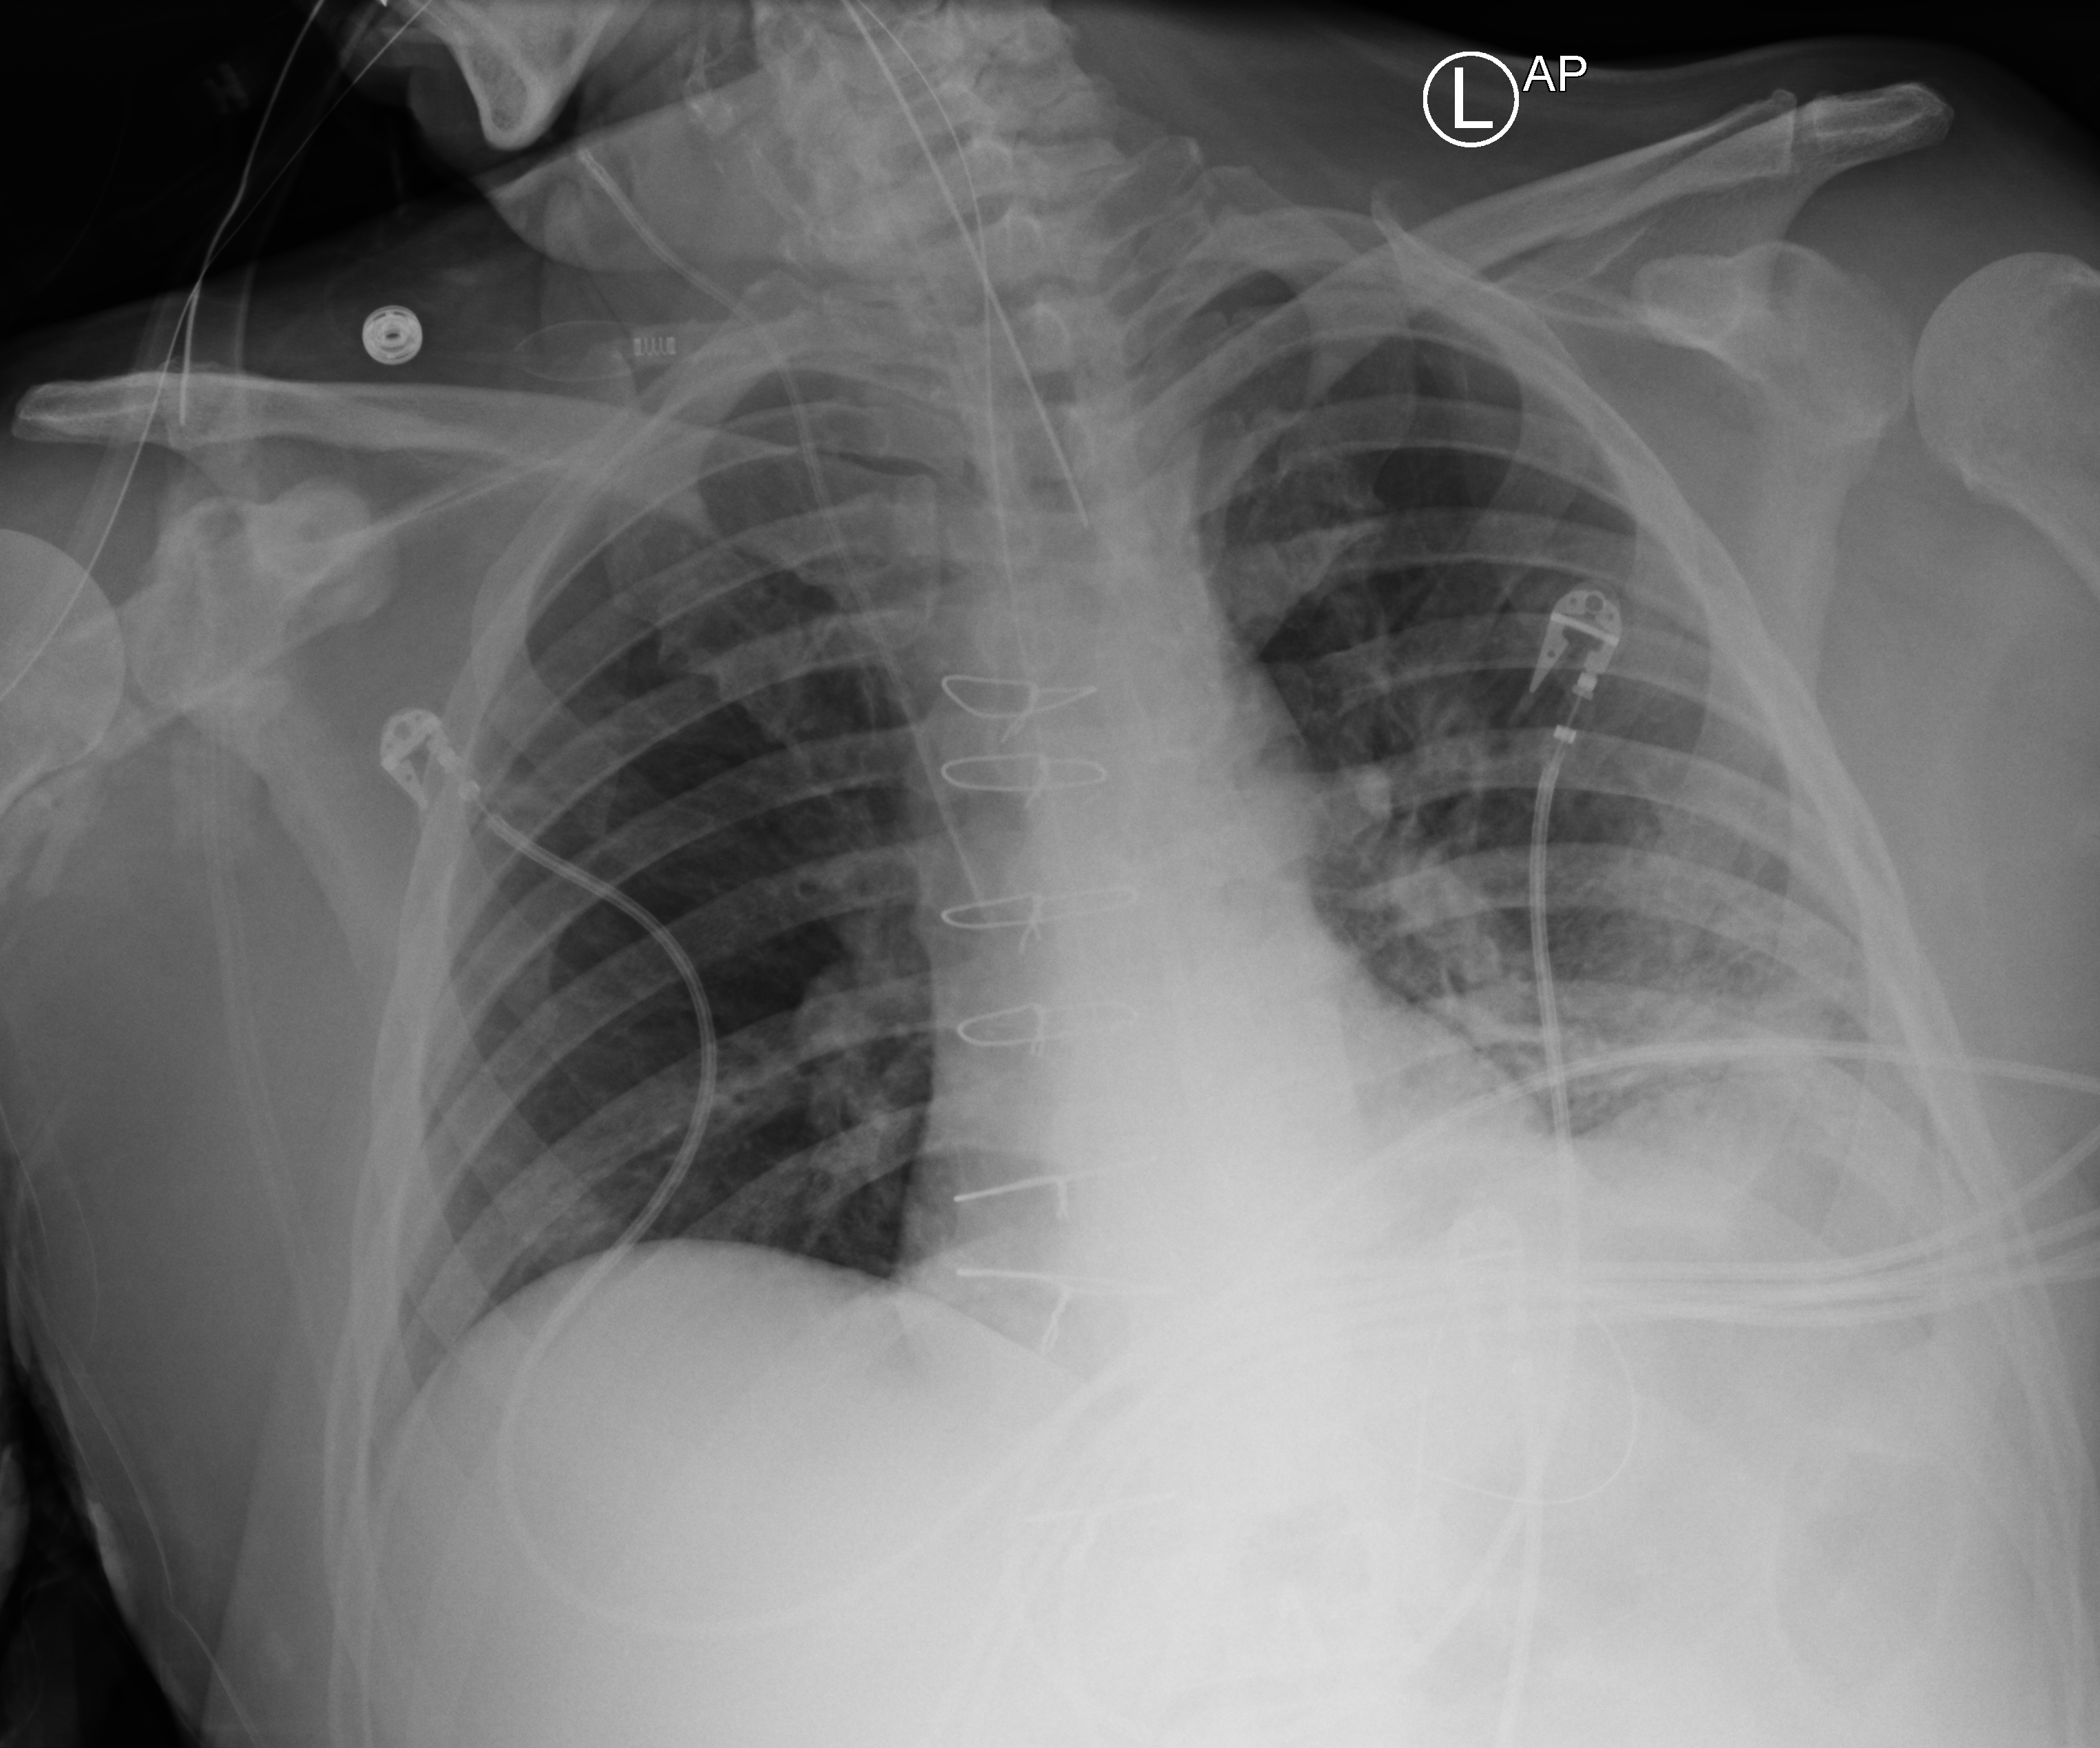
Portable chest radiograph, anteroposterior (AP) projection. Male patient hospitalised with COVID-19, age 60–74 years.
From the hospital-stay record, not from the radiograph (when in the stay this image was taken is not recorded): mechanically ventilated during this hospital stay: yes.